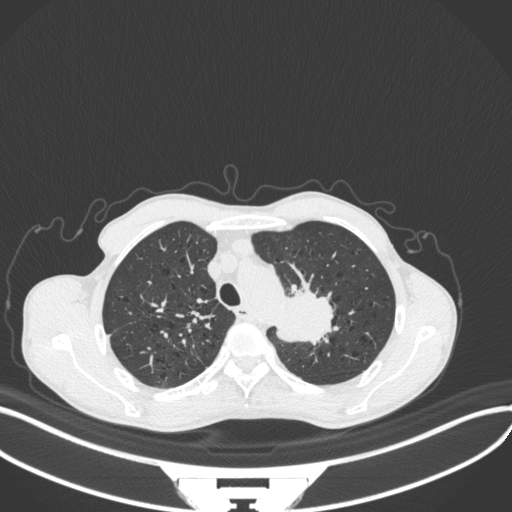
Chest CT, one axial slice; slice 333 of 394 in the series (ordered by position); reconstruction kernel B31f; 120 kVp; lung window (W 1500 / L -600 HU); 1 mm slice thickness; 512 × 512 image matrix, field of view 400 × 400 mm. Patient: male, 65 years. From the clinical record (not read from this slice): clinical TNM (as recorded): T2b N0 M0; histopathological grade: G2.
Structures marked on this image (bounding box drawn by a radiologist):
- lung tumour (recorded histology: adenocarcinoma): bounding box (x1, y1, x2, y2) in pixels: (272, 283, 340, 344)